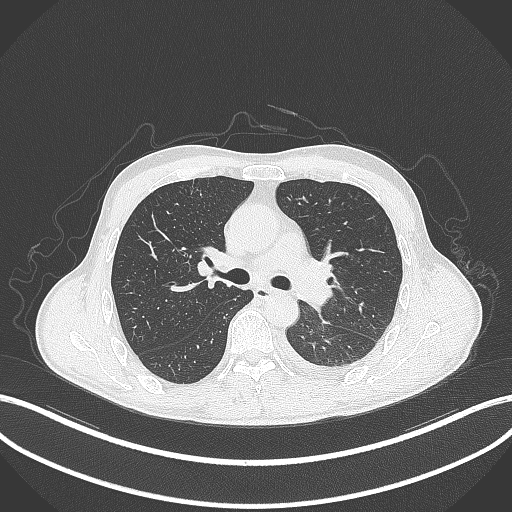
Chest CT, one axial slice. Position 205 of 295 along the scan axis. Reconstruction kernel B70f. Lung window (W 1500 / L -600 HU). 1 mm slice thickness. 512 × 512 image matrix, field of view 400 × 400 mm. Patient: male, 47 years. Case-level facts recorded for this patient, not image findings: clinical TNM (as recorded): T3 N1 M1c; histopathological grade: G3.
Annotated regions visible in this slice (rectangle marked by the reading radiologist):
- lung tumour (recorded histology: small cell carcinoma): bounding box <302,280,337,308> (left, top, right, bottom; pixels)